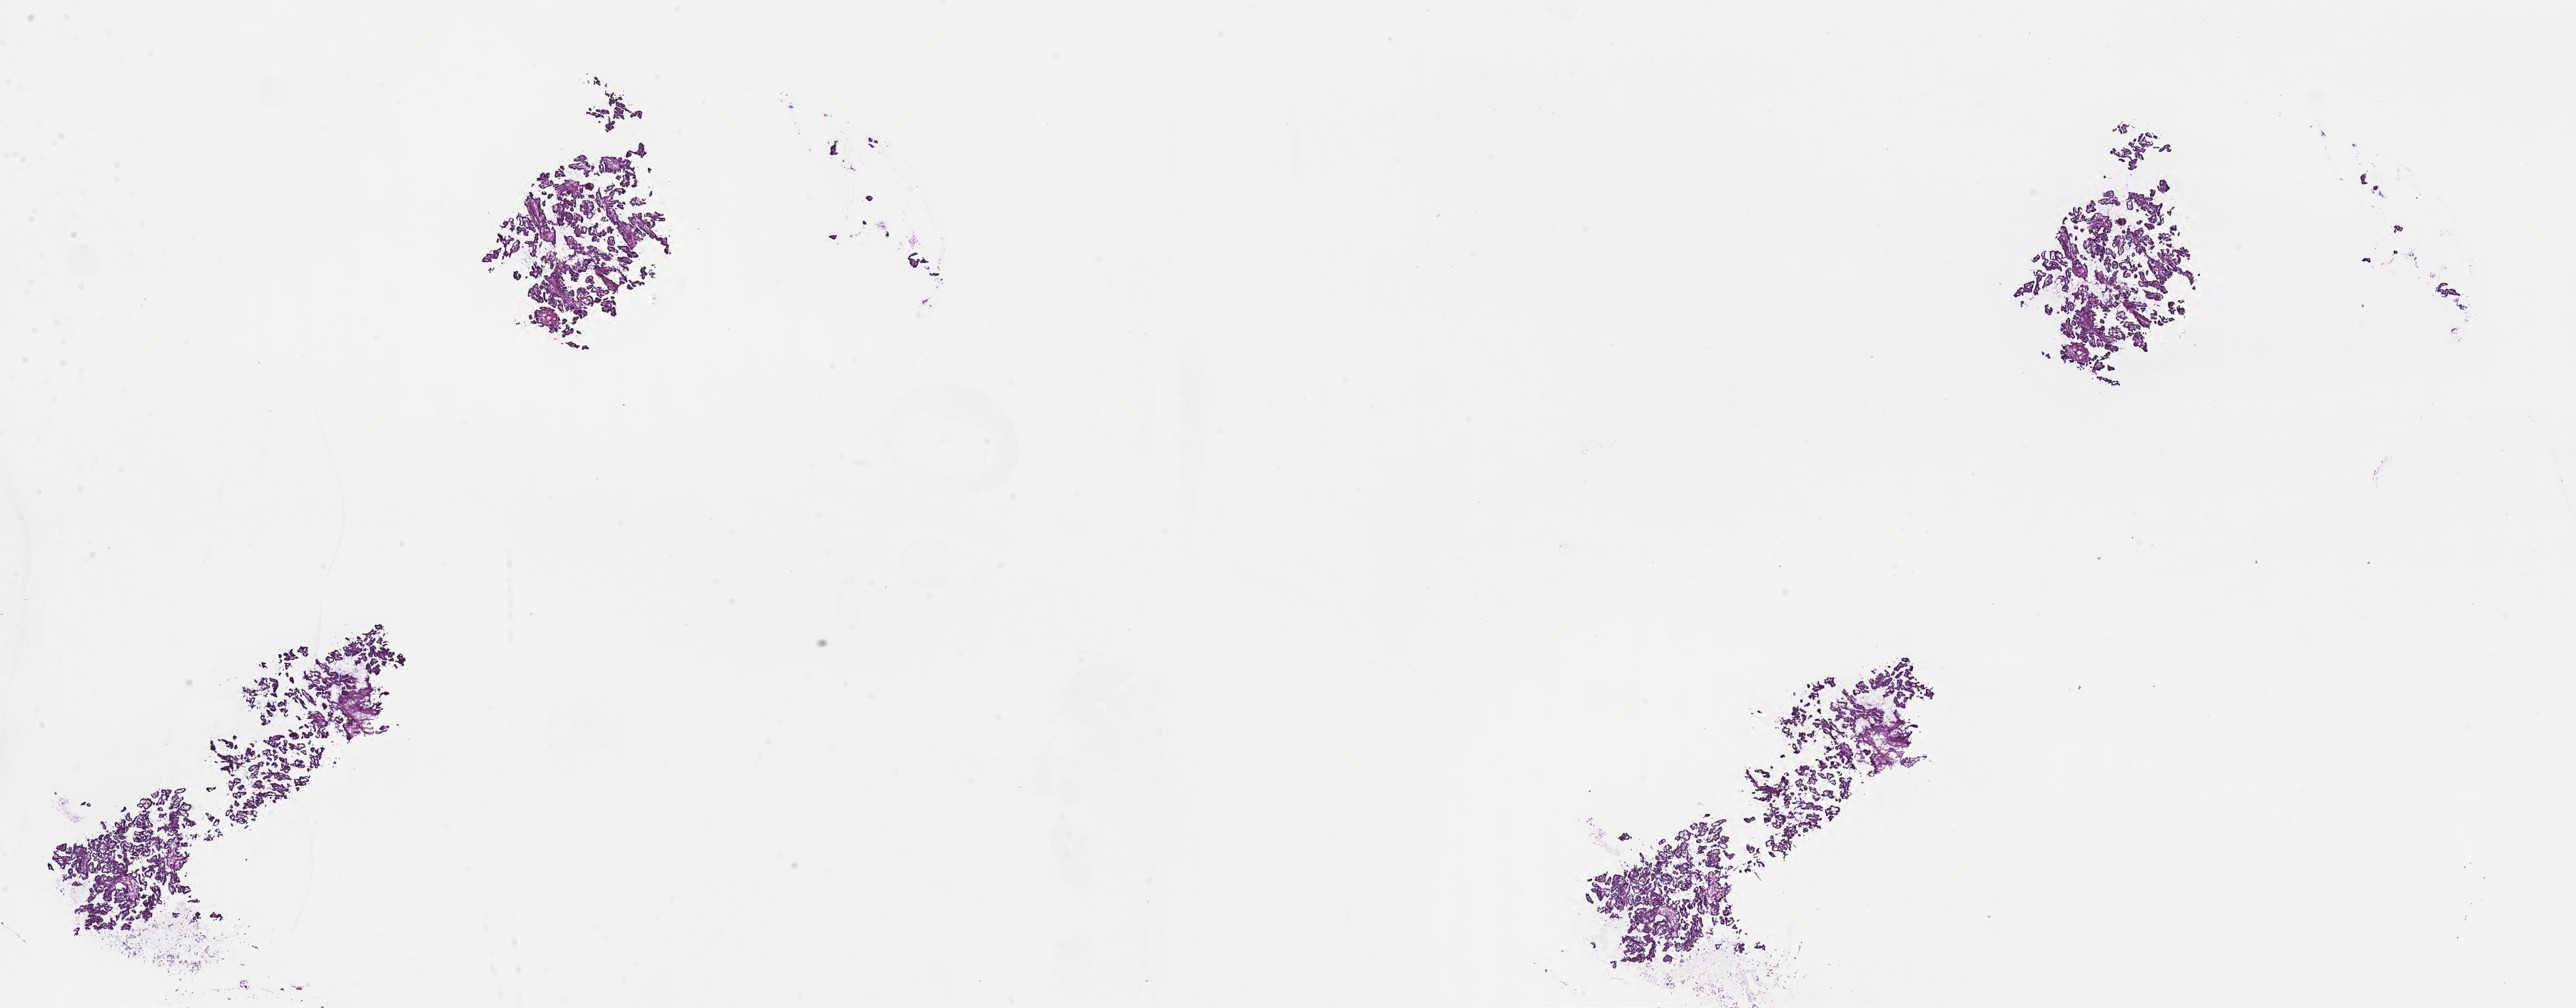
Digitized haematoxylin and eosin-stained section of tumor tissue from the cerebral ventricle — whole scanned area (about 29.2 x 11.4 mm) shown as a low-resolution overview; cryosection (OCT / tissue freezing medium). Patient: male, age 552 days (about 1.5 years).
Diagnosis (ICD-O-3 morphology term): Neoplasm, uncertain whether benign or malignant.